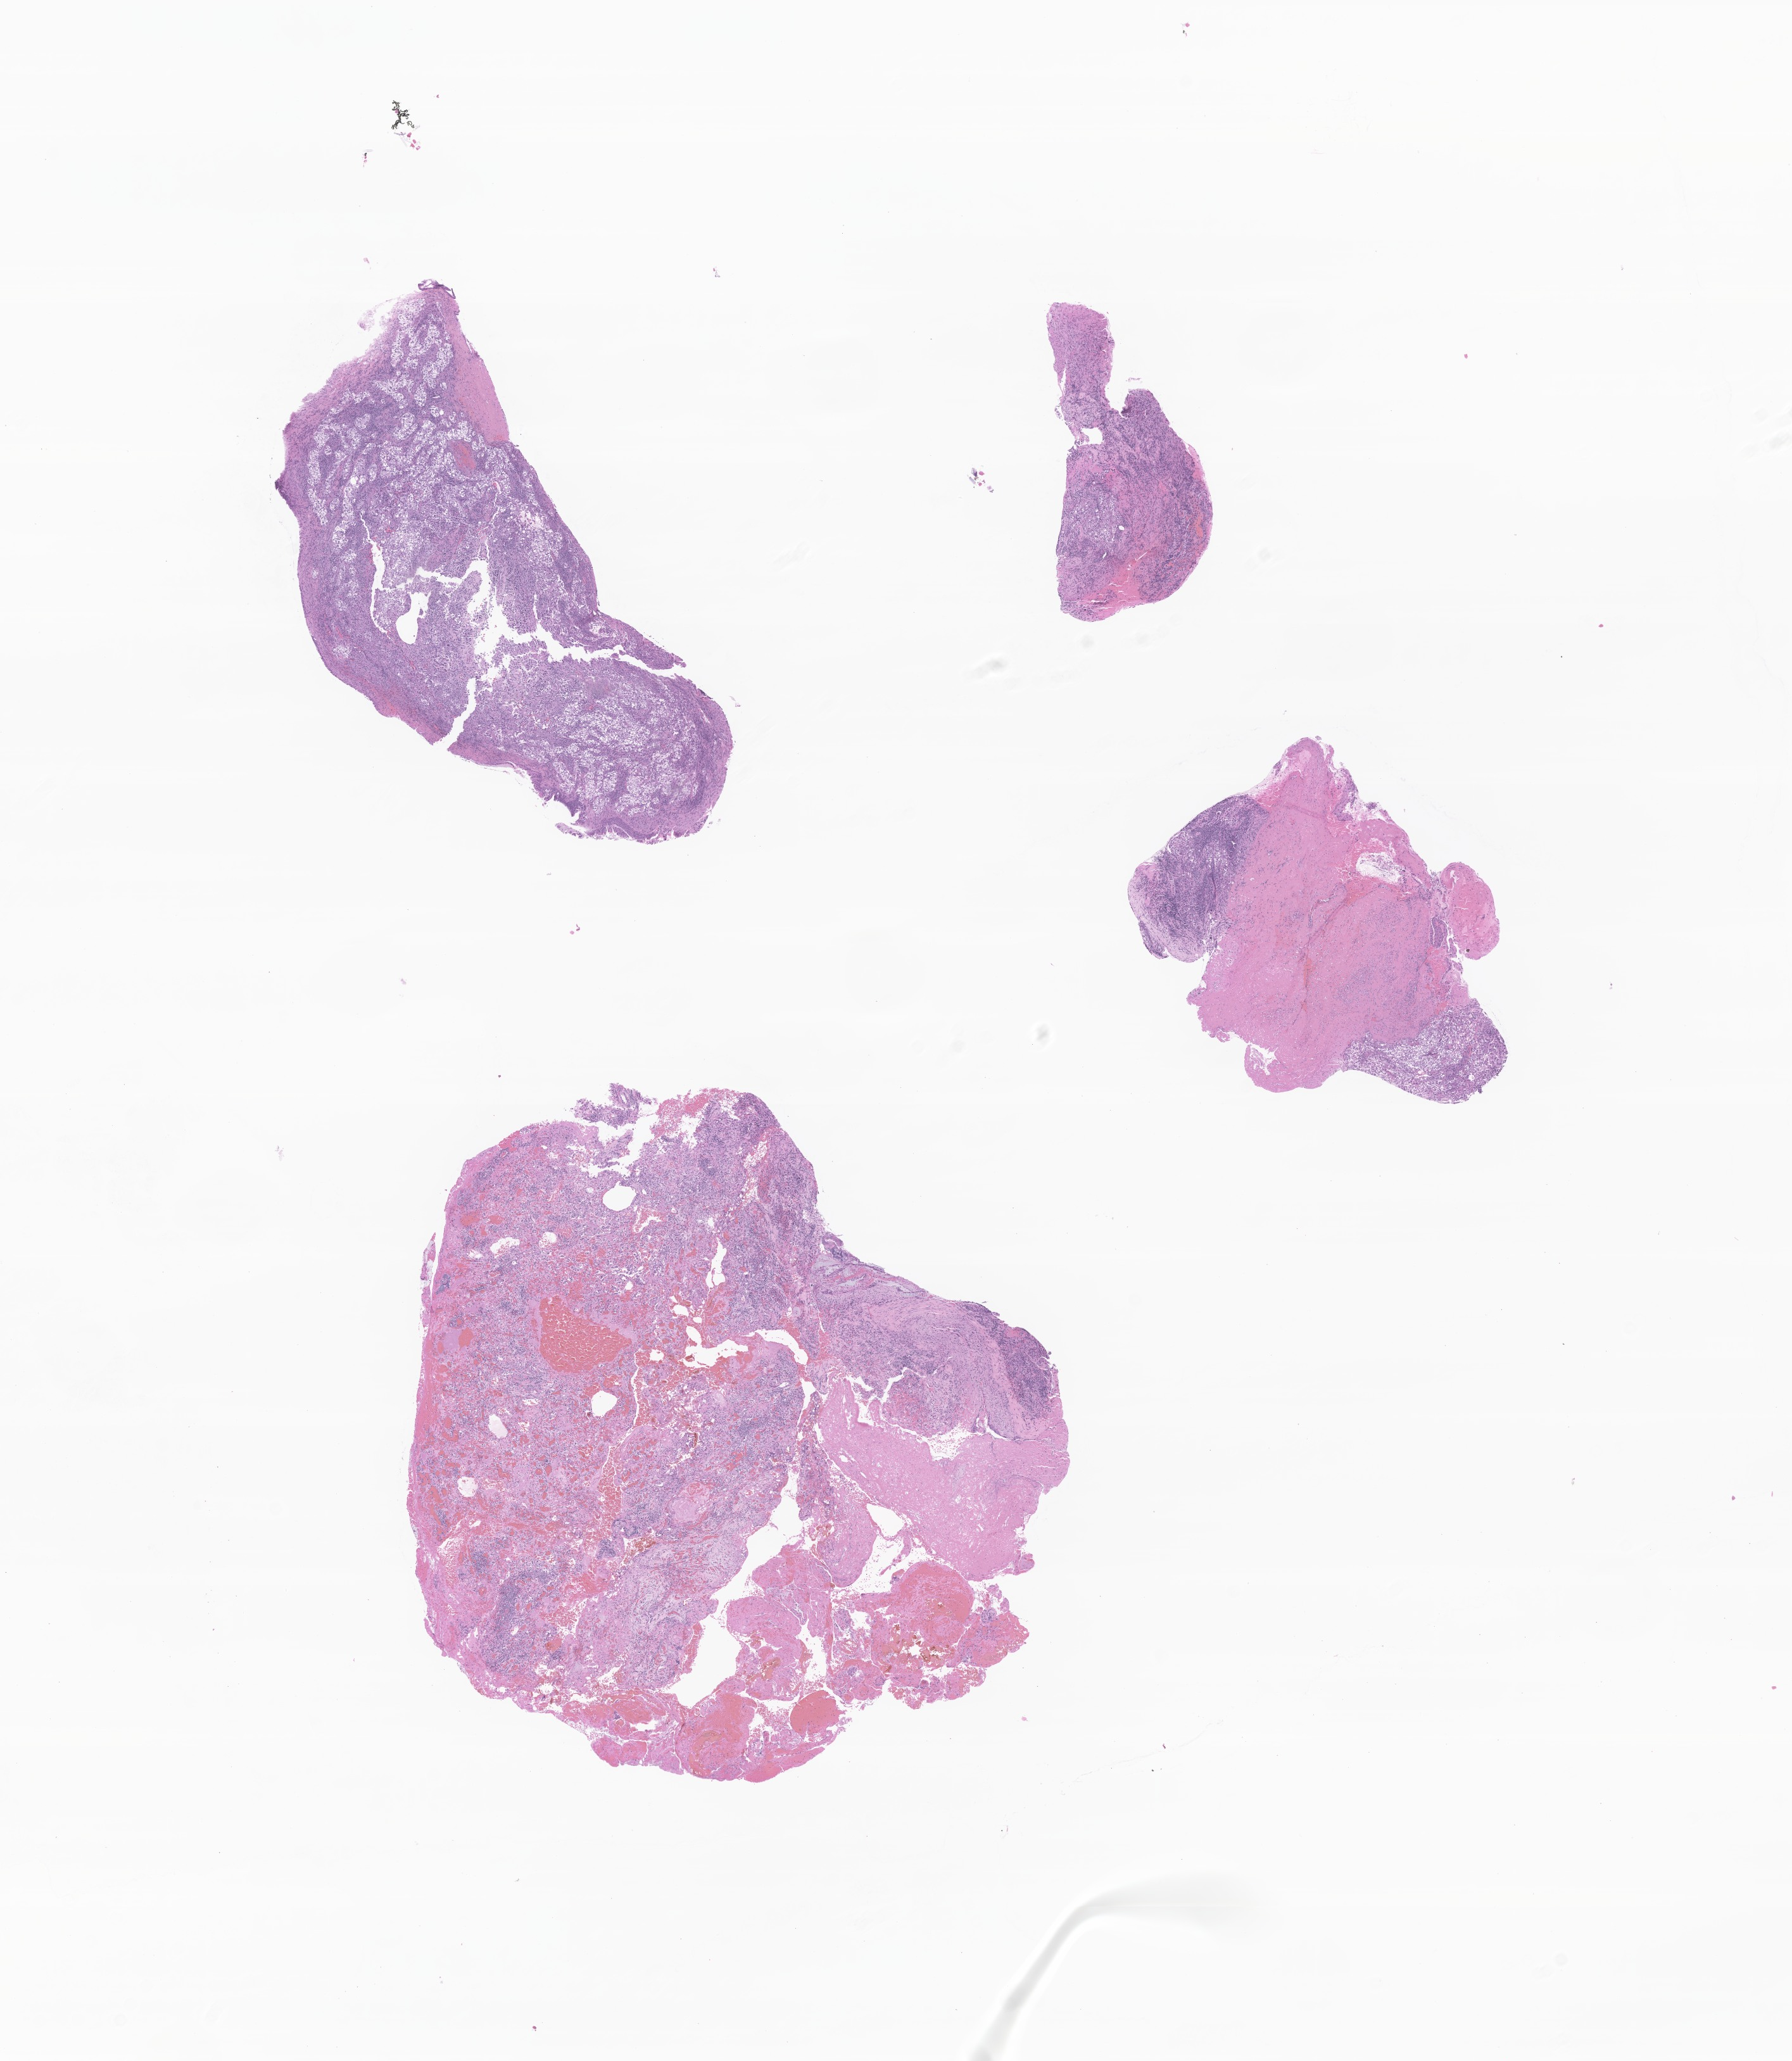
Whole-slide image, hematoxylin and eosin (H&E) stain of tumor tissue from the main bronchus, a low-resolution overview of the entire scanned area, about 11.9 x 13.7 mm, formalin-fixed paraffin-embedded section. Patient: female, age 162 months (13 years 6 months).
• diagnosis (ICD-O-3 morphology term): Mucoepidermoid carcinoma